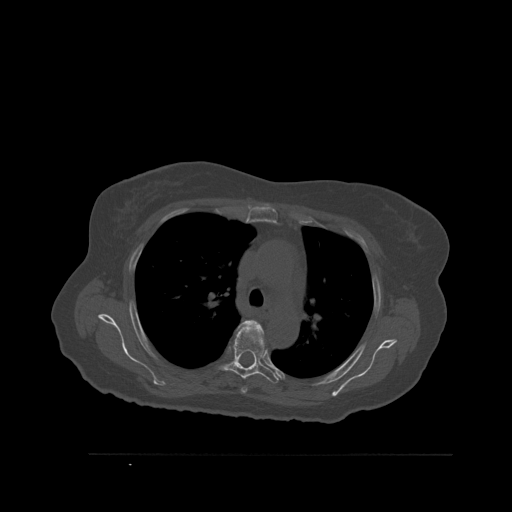
CT including the spine, one axial slice. Slice 397 of 527 in the series (ordered by position). Bone window (W 1800 / L 400 HU). 512 × 512 image matrix, field of view 470 × 470 mm. Female patient, age 73 years. From the clinical record (not read from this slice): primary cancer: breast; vertebrae with lytic lesions (as recorded): L2.
Annotated regions visible in this slice (semi-automatic segmentation, software-assisted and operator-edited):
- T4 vertebra: bounding box [x1, y1, x2, y2] px = [239, 319, 265, 394]
- T5 vertebra: [221, 328, 280, 384]